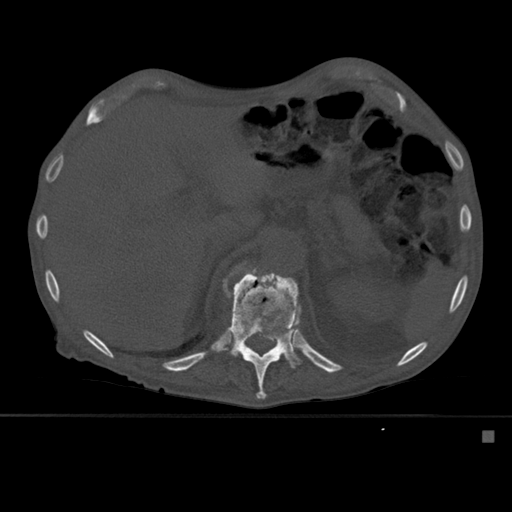
CT including the spine, one axial slice. Position 275 of 527 along the scan axis. Bone window (W 1800 / L 400 HU). 1.5 mm slice thickness. 512 × 512 image matrix, field of view 373 × 373 mm. Patient: male, 78 years. From the clinical record (not read from this slice): primary cancer: prostate.
Annotated regions visible in this slice (semi-automatically segmented with operator editing):
- T12 vertebra: bounding box <223,268,302,400> (left, top, right, bottom; pixels)